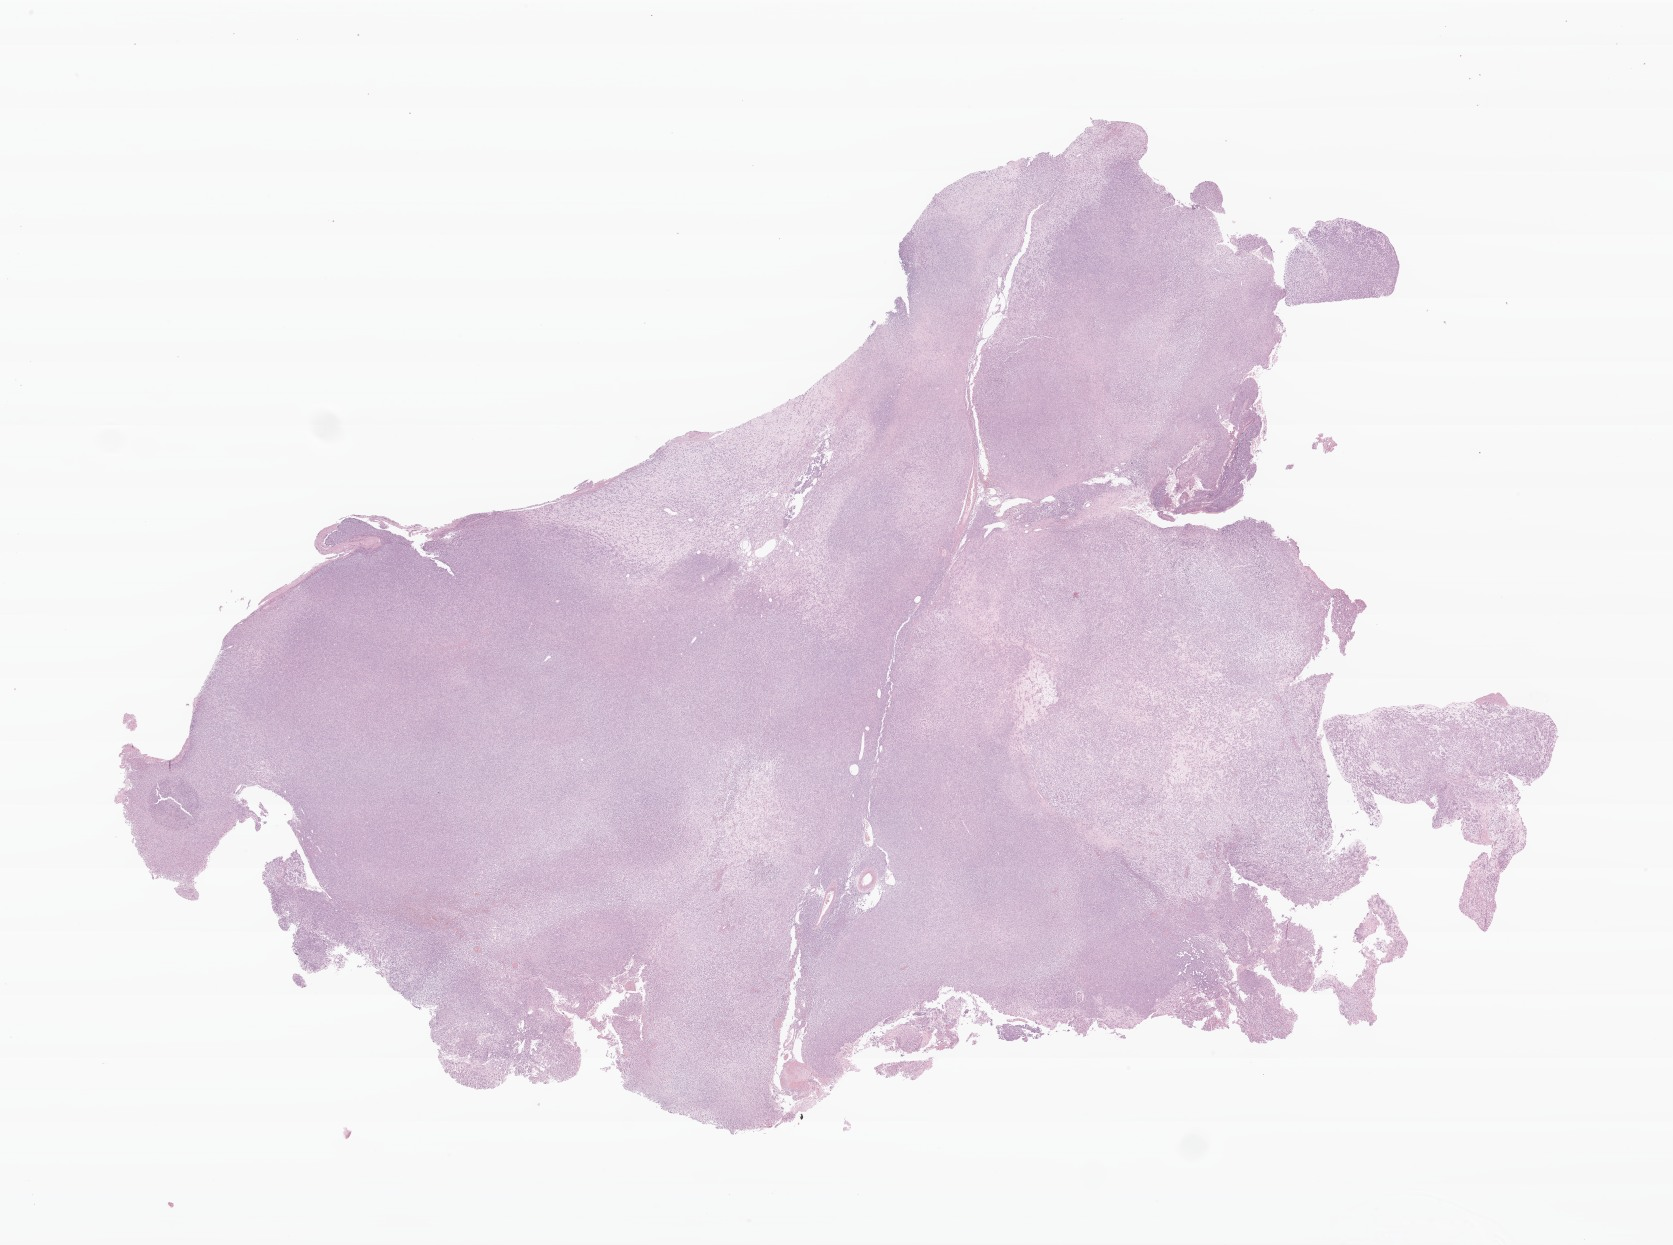
Hematoxylin and eosin (H&E) whole-slide image of tumor tissue from the brain, shown as a low-resolution overview of the whole scanned area (about 28.1 x 20.9 mm); formalin-fixed, paraffin-embedded (FFPE) tissue. Patient male; age 820 days (about 2.2 years).
Diagnosis: Atypical teratoid/rhabdoid tumor.